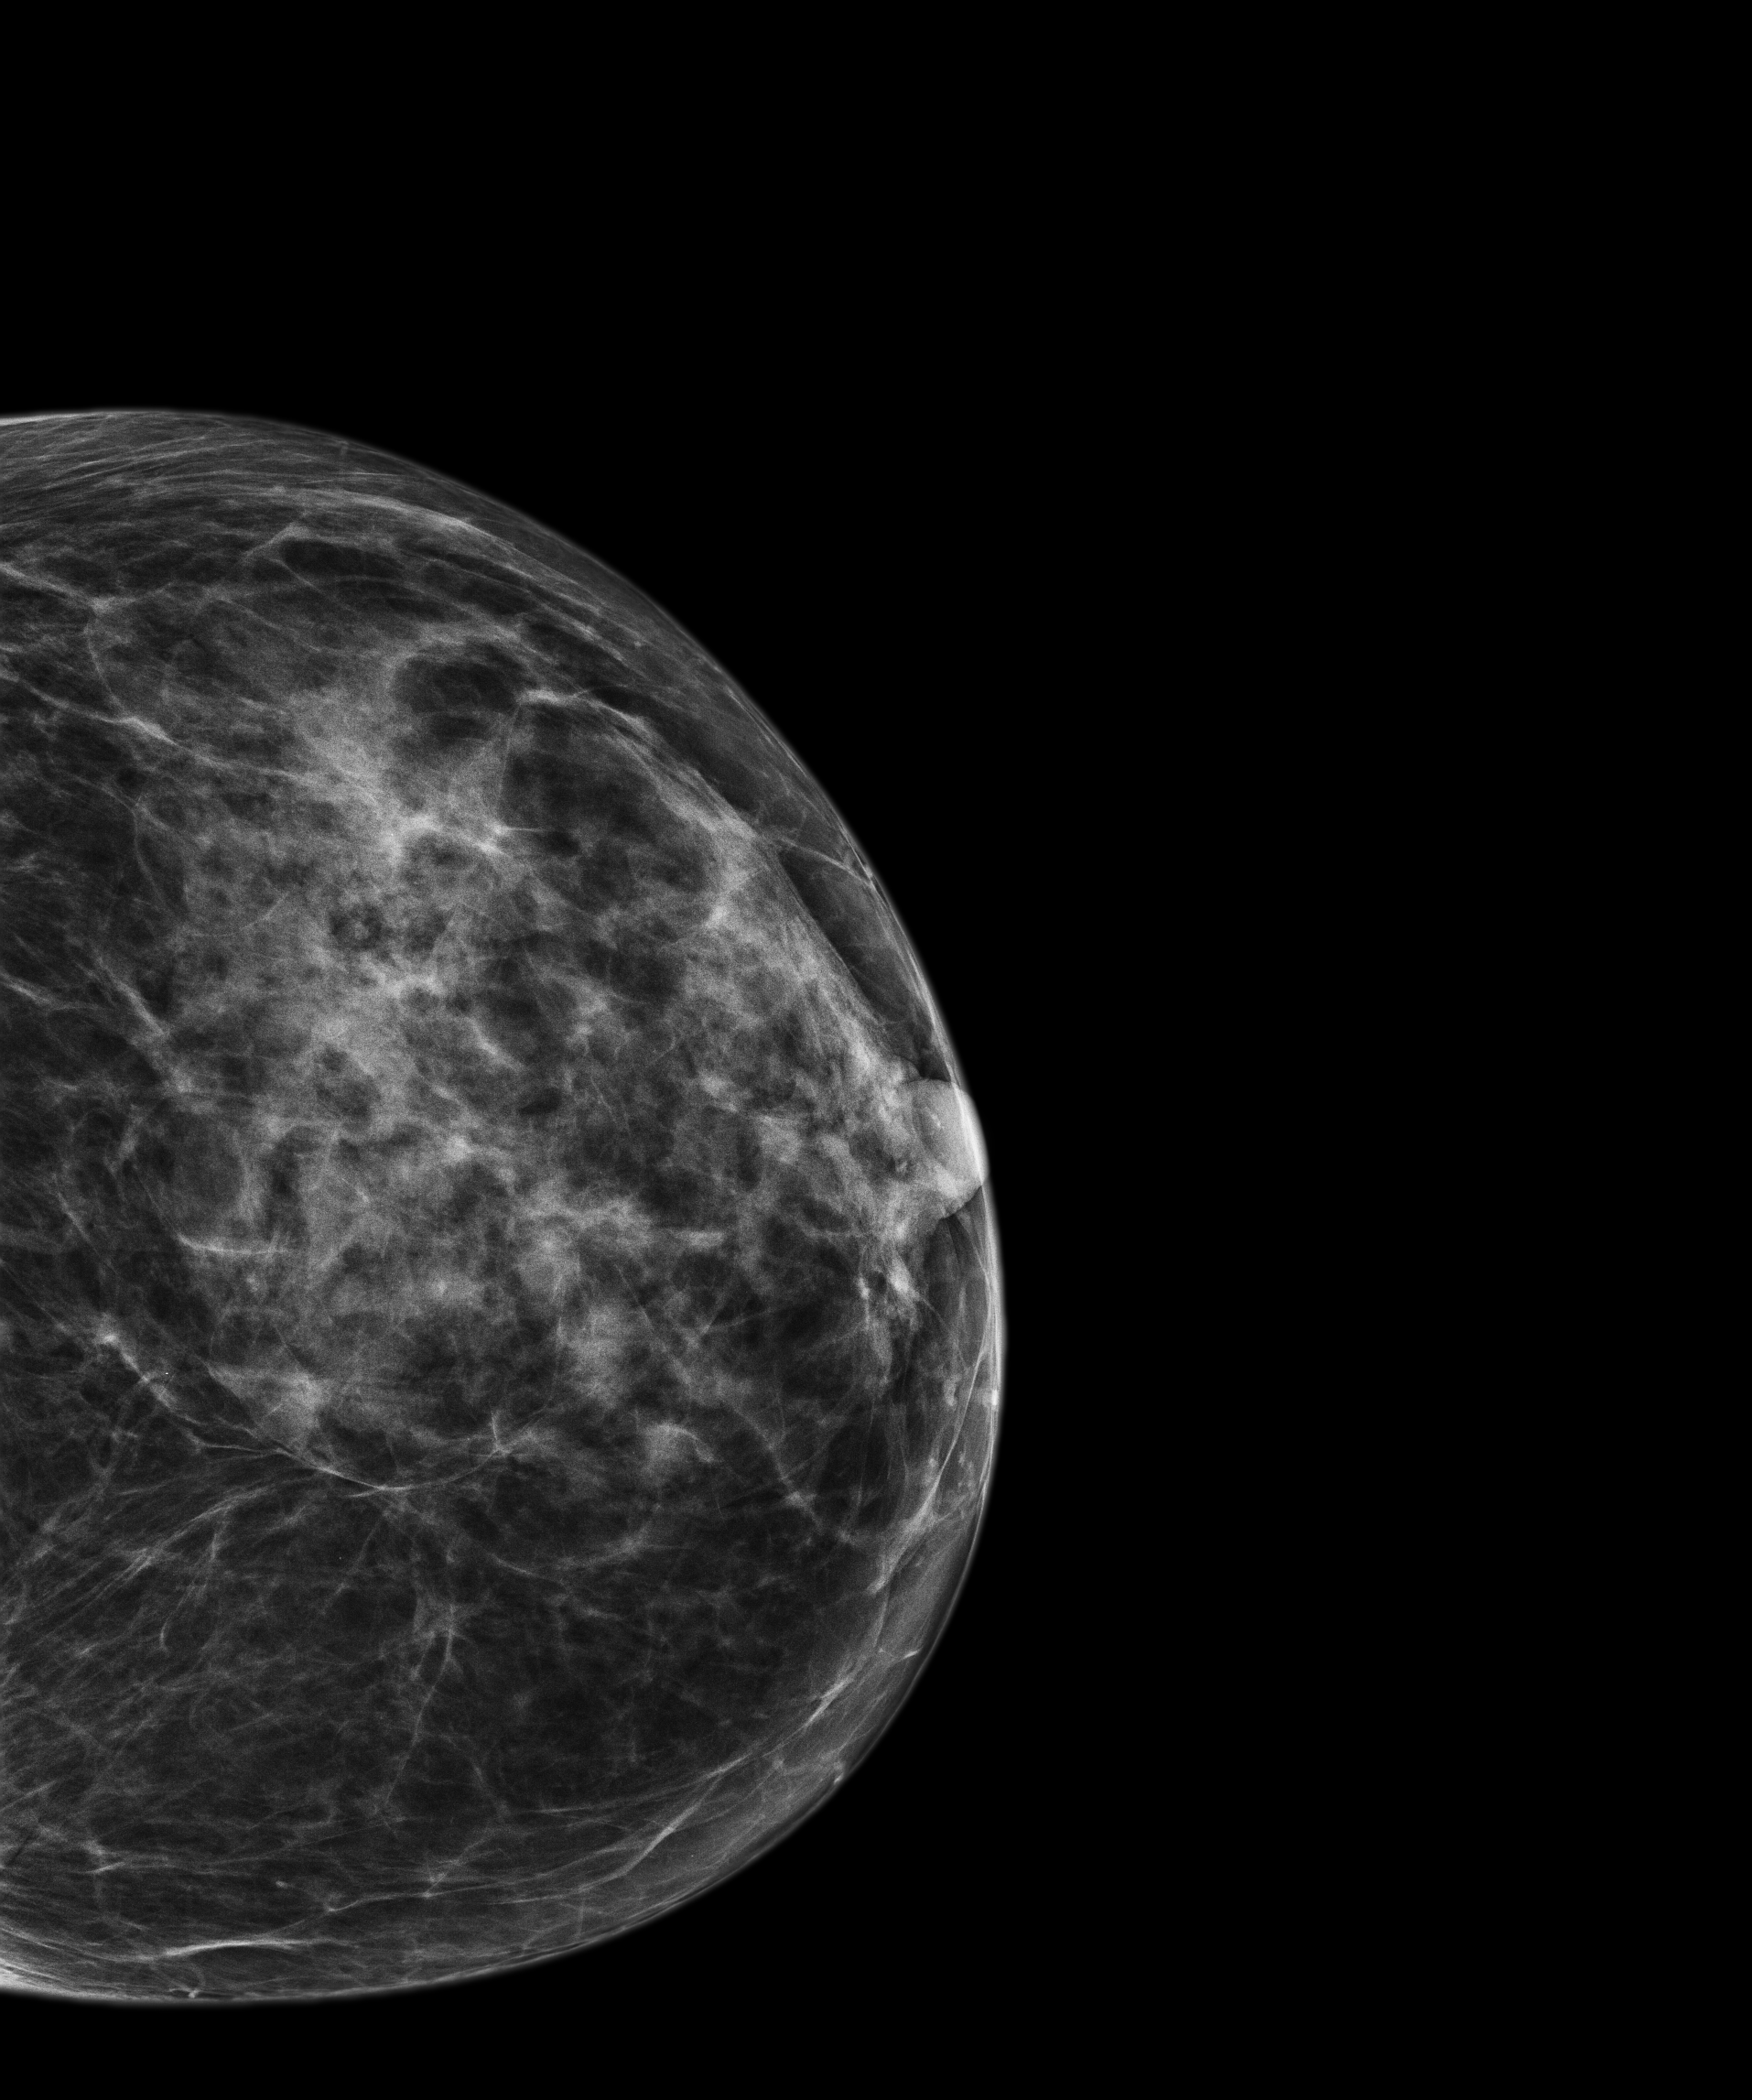
Annual screening mammography examination; compressed breast thickness 34.5 mm. Female patient, age 57 years.
Image type: full-field digital mammogram. Breast: left. Projection: CC view.